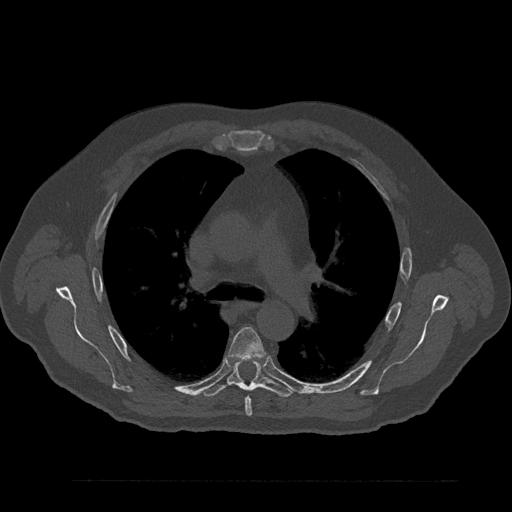
CT including the spine, one axial slice; slice 578 of 797 in the series (ordered by position); reconstruction kernel Br40s/3; 120 kVp; bone window (W 1800 / L 400 HU); 512 × 512 image matrix. Patient: male, 61 years. From the clinical record (not read from this slice): primary cancer: prostate.
Annotated regions visible in this slice (semi-automatically segmented with operator editing):
- T5 vertebra: box from (x=228, y=327) to (x=266, y=416) px
- T6 vertebra: (x=203, y=359)–(x=293, y=397)